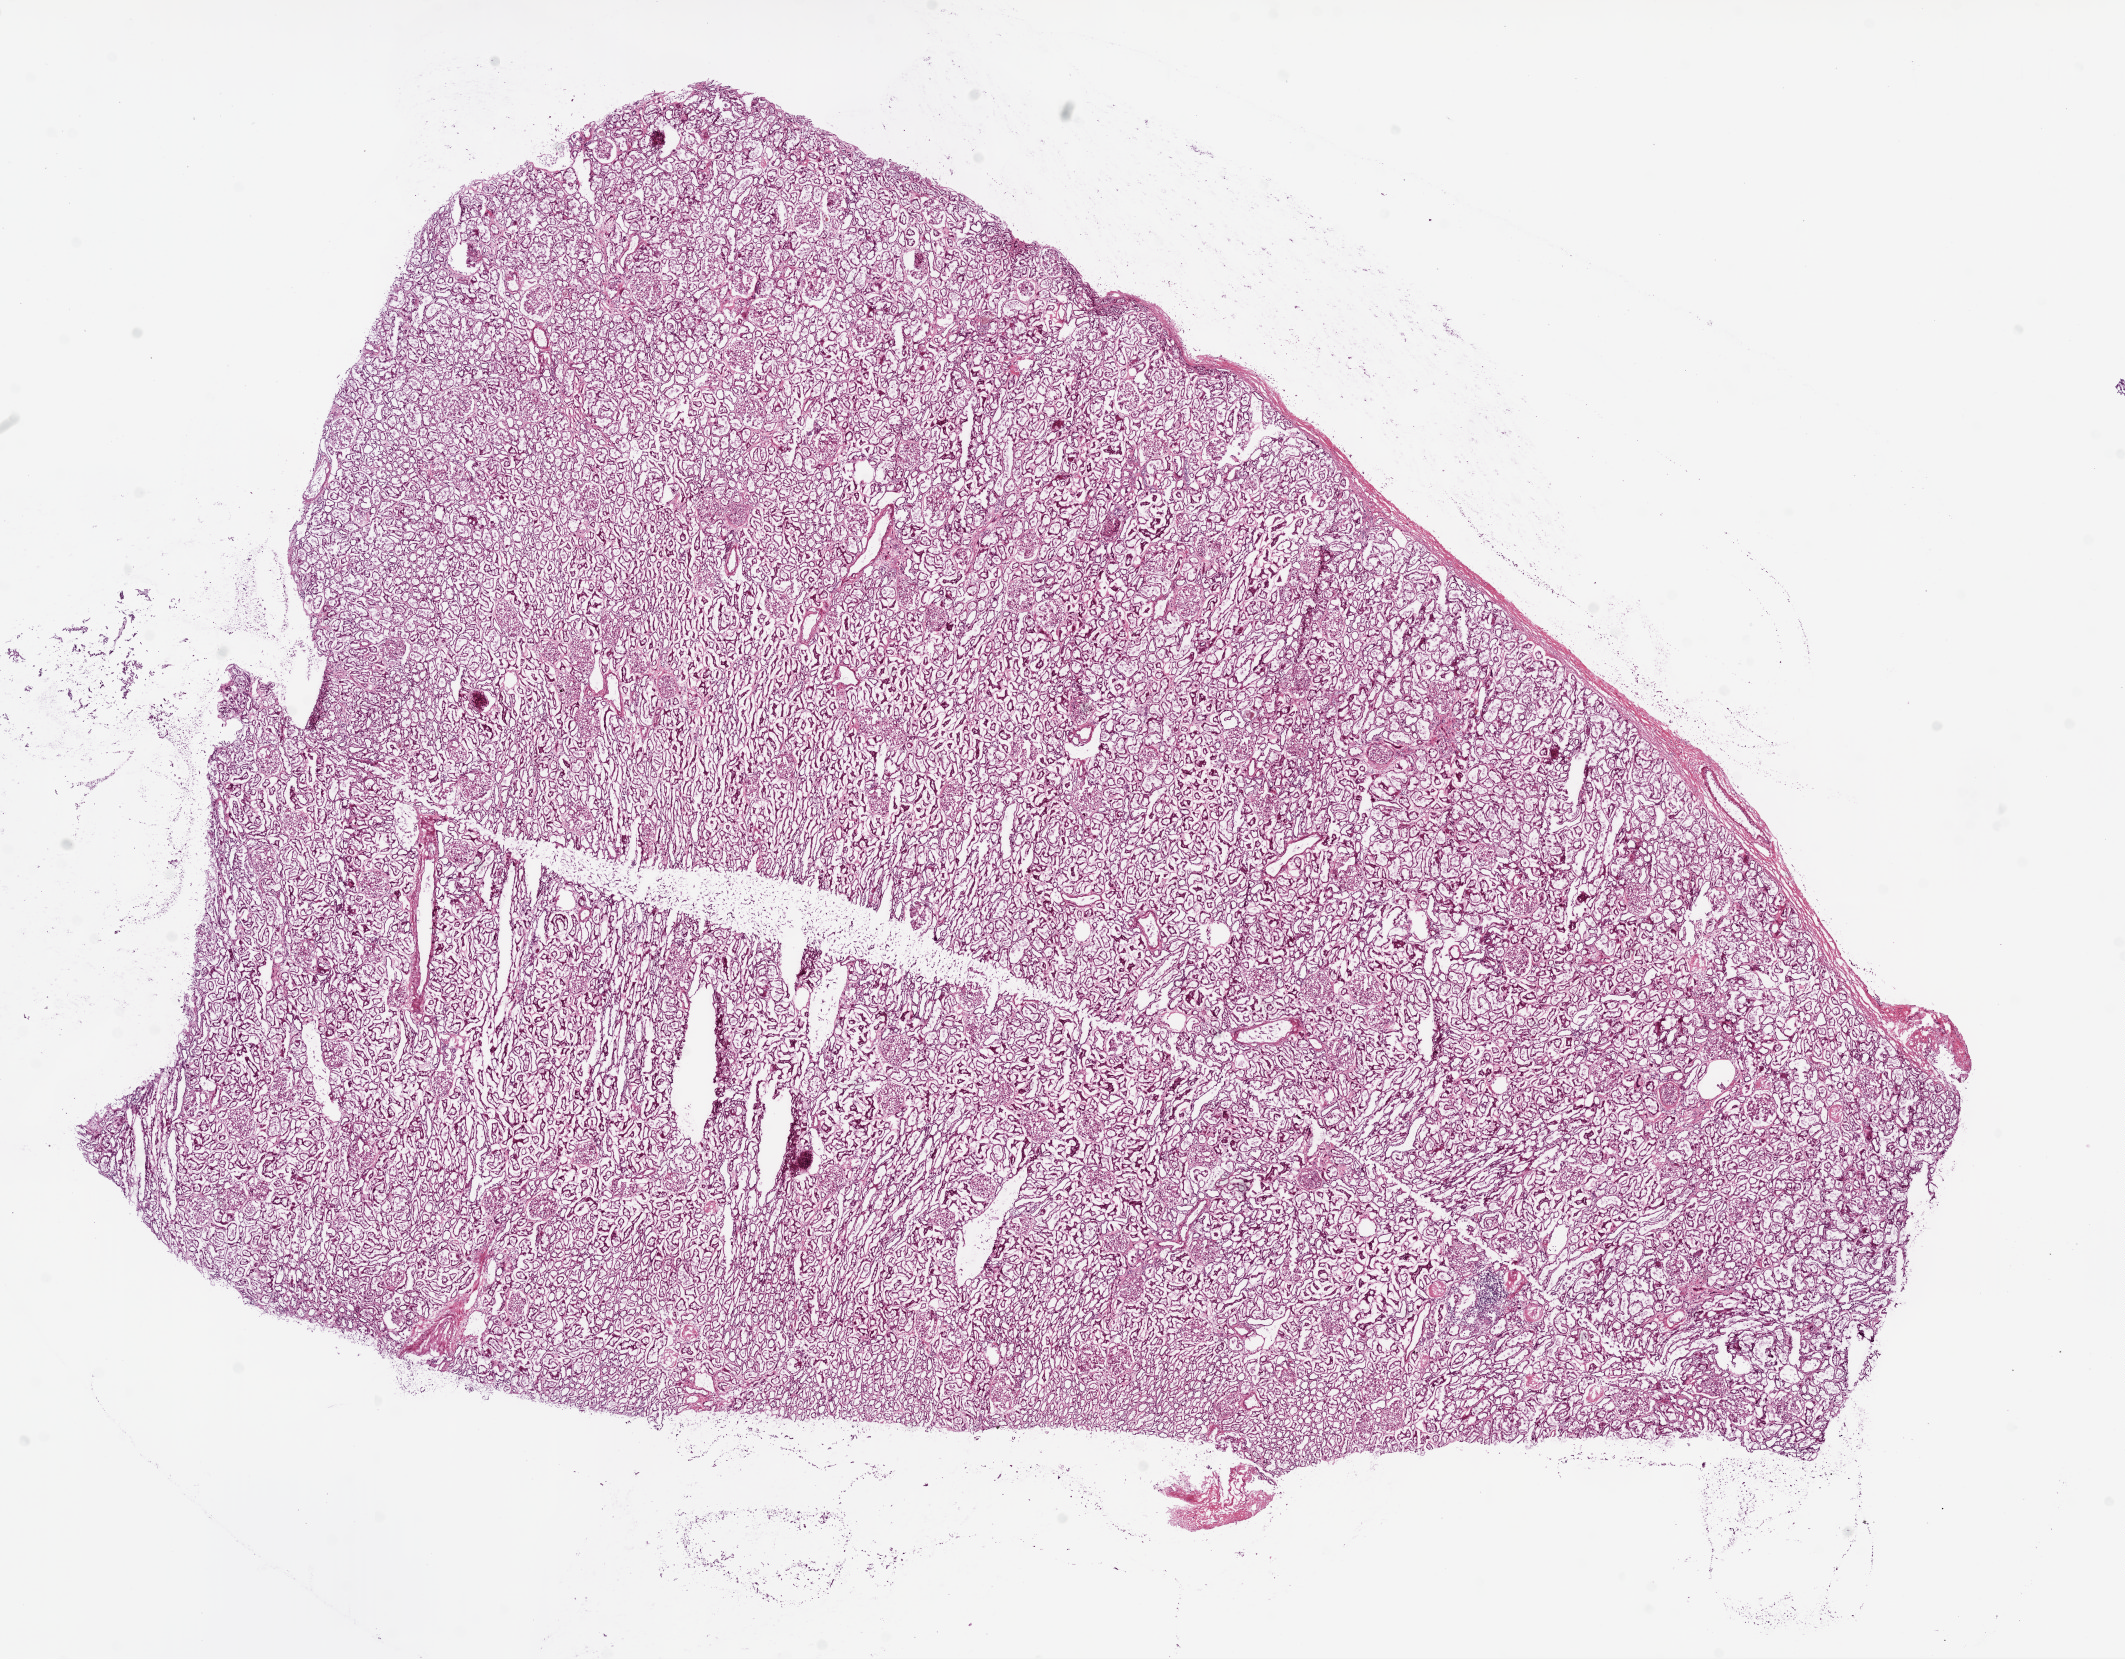
H&E whole-slide image — shown as a low-resolution overview of the whole scanned area (about 17.1 x 13.3 mm). Frozen section from the bottom of the tissue portion. Solid tissue normal (non-tumour tissue) sample from the kidney. Patient: male, age at initial diagnosis 61 years.
• this section: solid tissue normal sample (biorepository sample class)
• patient diagnosis: Clear cell adenocarcinoma, NOS